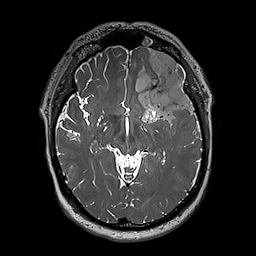
Brain MRI from a brain-tumour surgery series, one axial slice. Slice 120 of 192 in the series (ordered by position). 1 mm slice thickness. 256 × 256 image matrix, field of view 250 × 250 mm. Case-level facts recorded for this patient, not image findings: histopathology: Oligodendroglioma; WHO grade: 3; IDH mutation: yes.
Annotated regions visible in this slice (expert manual segmentation):
- tumour: bounding box [x1, y1, x2, y2] px = [124, 50, 197, 123]